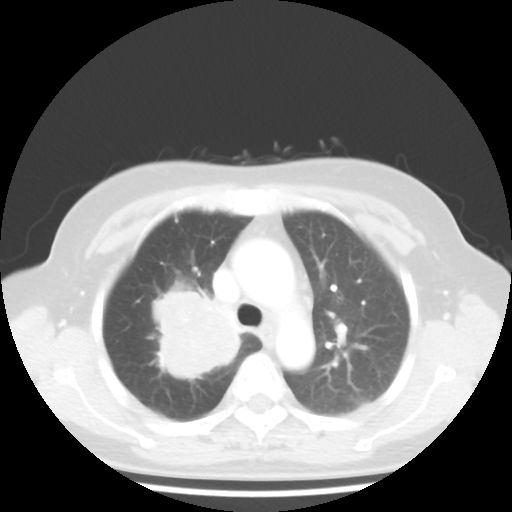
Chest CT, one axial slice. Slice 31 of 44 in the series (ordered by position). 100 kVp. Lung window (W 1500 / L -600 HU). 5 mm slice thickness. 512 × 512 image matrix, field of view 316 × 316 mm. Patient: female, 62 years. From the clinical record (not read from this slice): clinical TNM (as recorded): T3 N0 M0; histopathological grade: G3.
Structures marked on this image (bounding box drawn by a radiologist):
- lung tumour (recorded histology: small cell carcinoma): box from (x=139, y=283) to (x=250, y=384) px